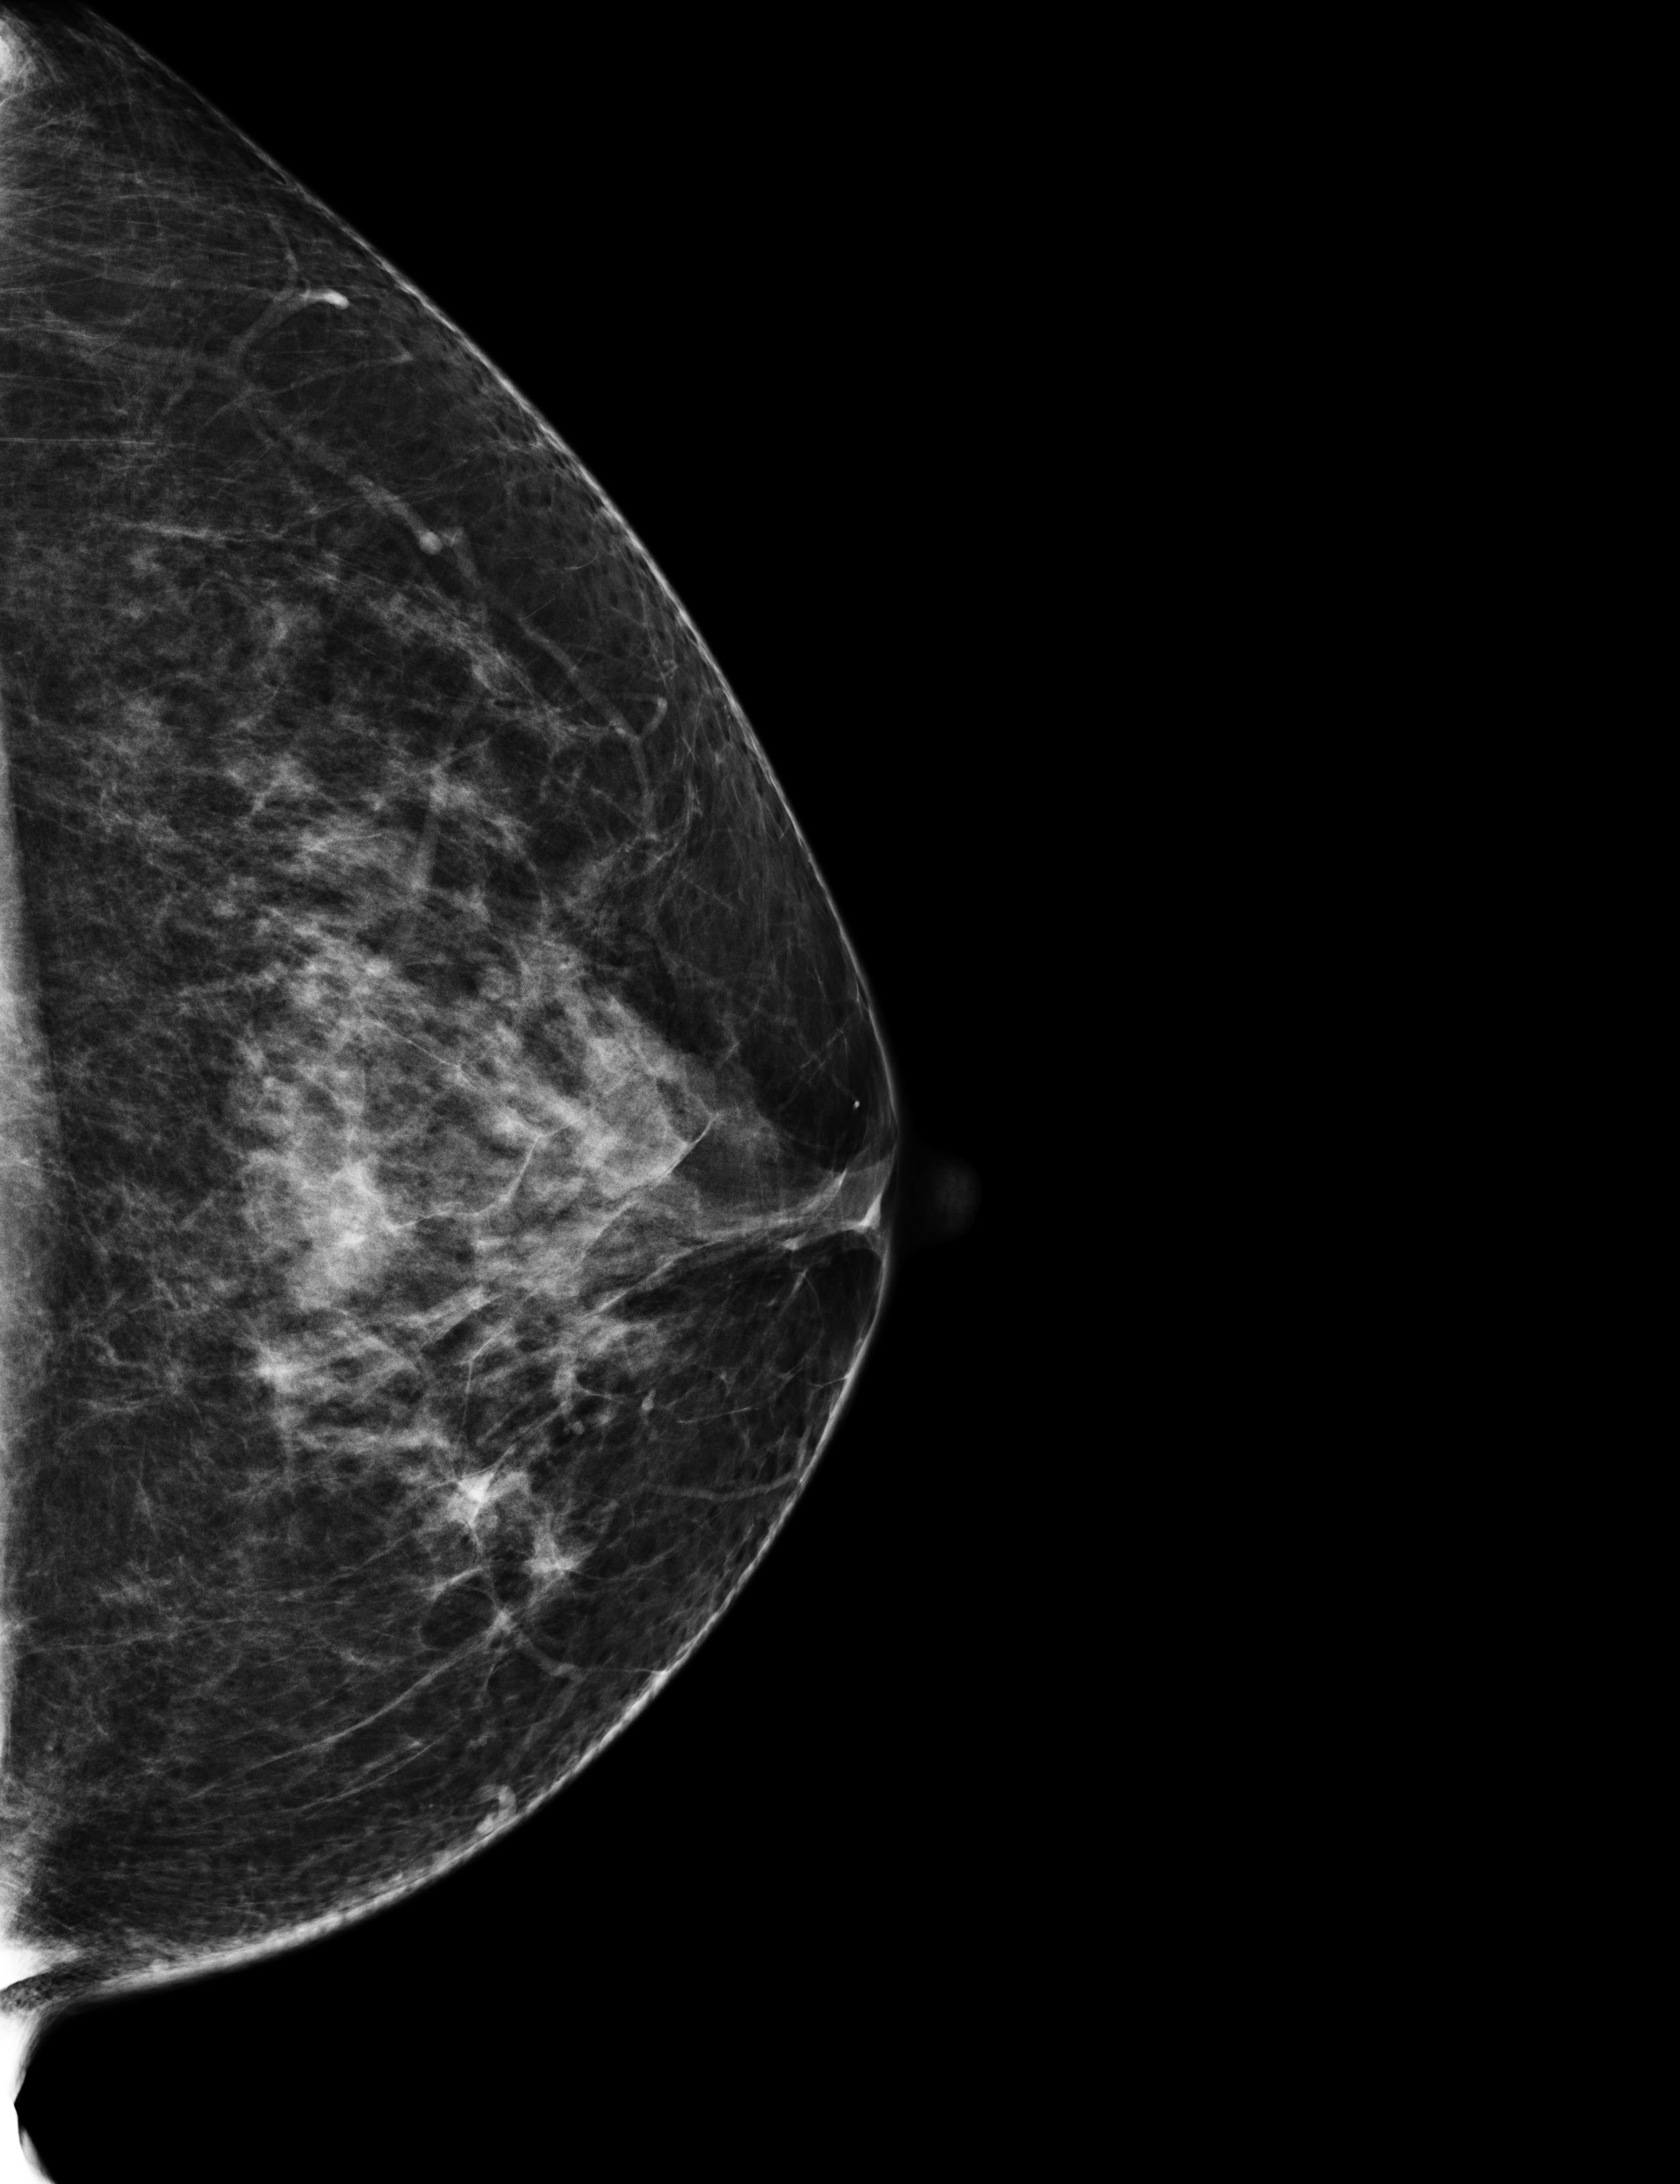
Digital mammogram (FFDM), left breast, CC view, screening examination, system: Selenia Dimensions. Patient aged 53 years (female).
Breast density at the screening exam (both breasts): heterogeneously dense (BI-RADS density category c). Final BI-RADS category for the screening round (tomosynthesis exam, both breasts): category 1. Recall: no recall after this screen.